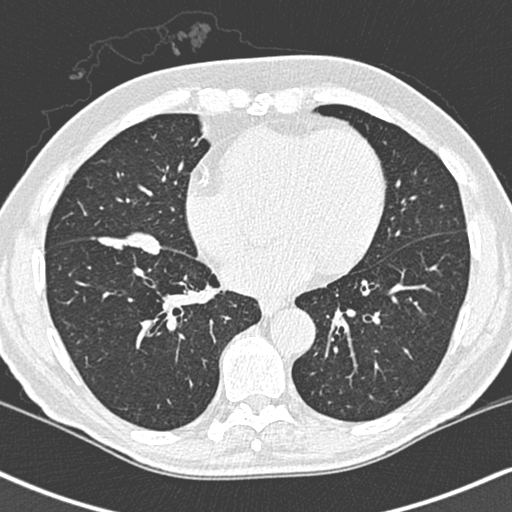
Low-dose screening chest CT, one axial slice; slice 108 of 248 in the series (ordered by position); 120 kVp; lung window (W 1500 / L -600 HU); 512 × 512 image matrix, field of view 323 × 323 mm.
Structures marked on this image (expert manual segmentation):
- lesion 1 (tumor, lower lobe of right lung): bounding box (x1, y1, x2, y2) in pixels: (98, 194, 163, 230)